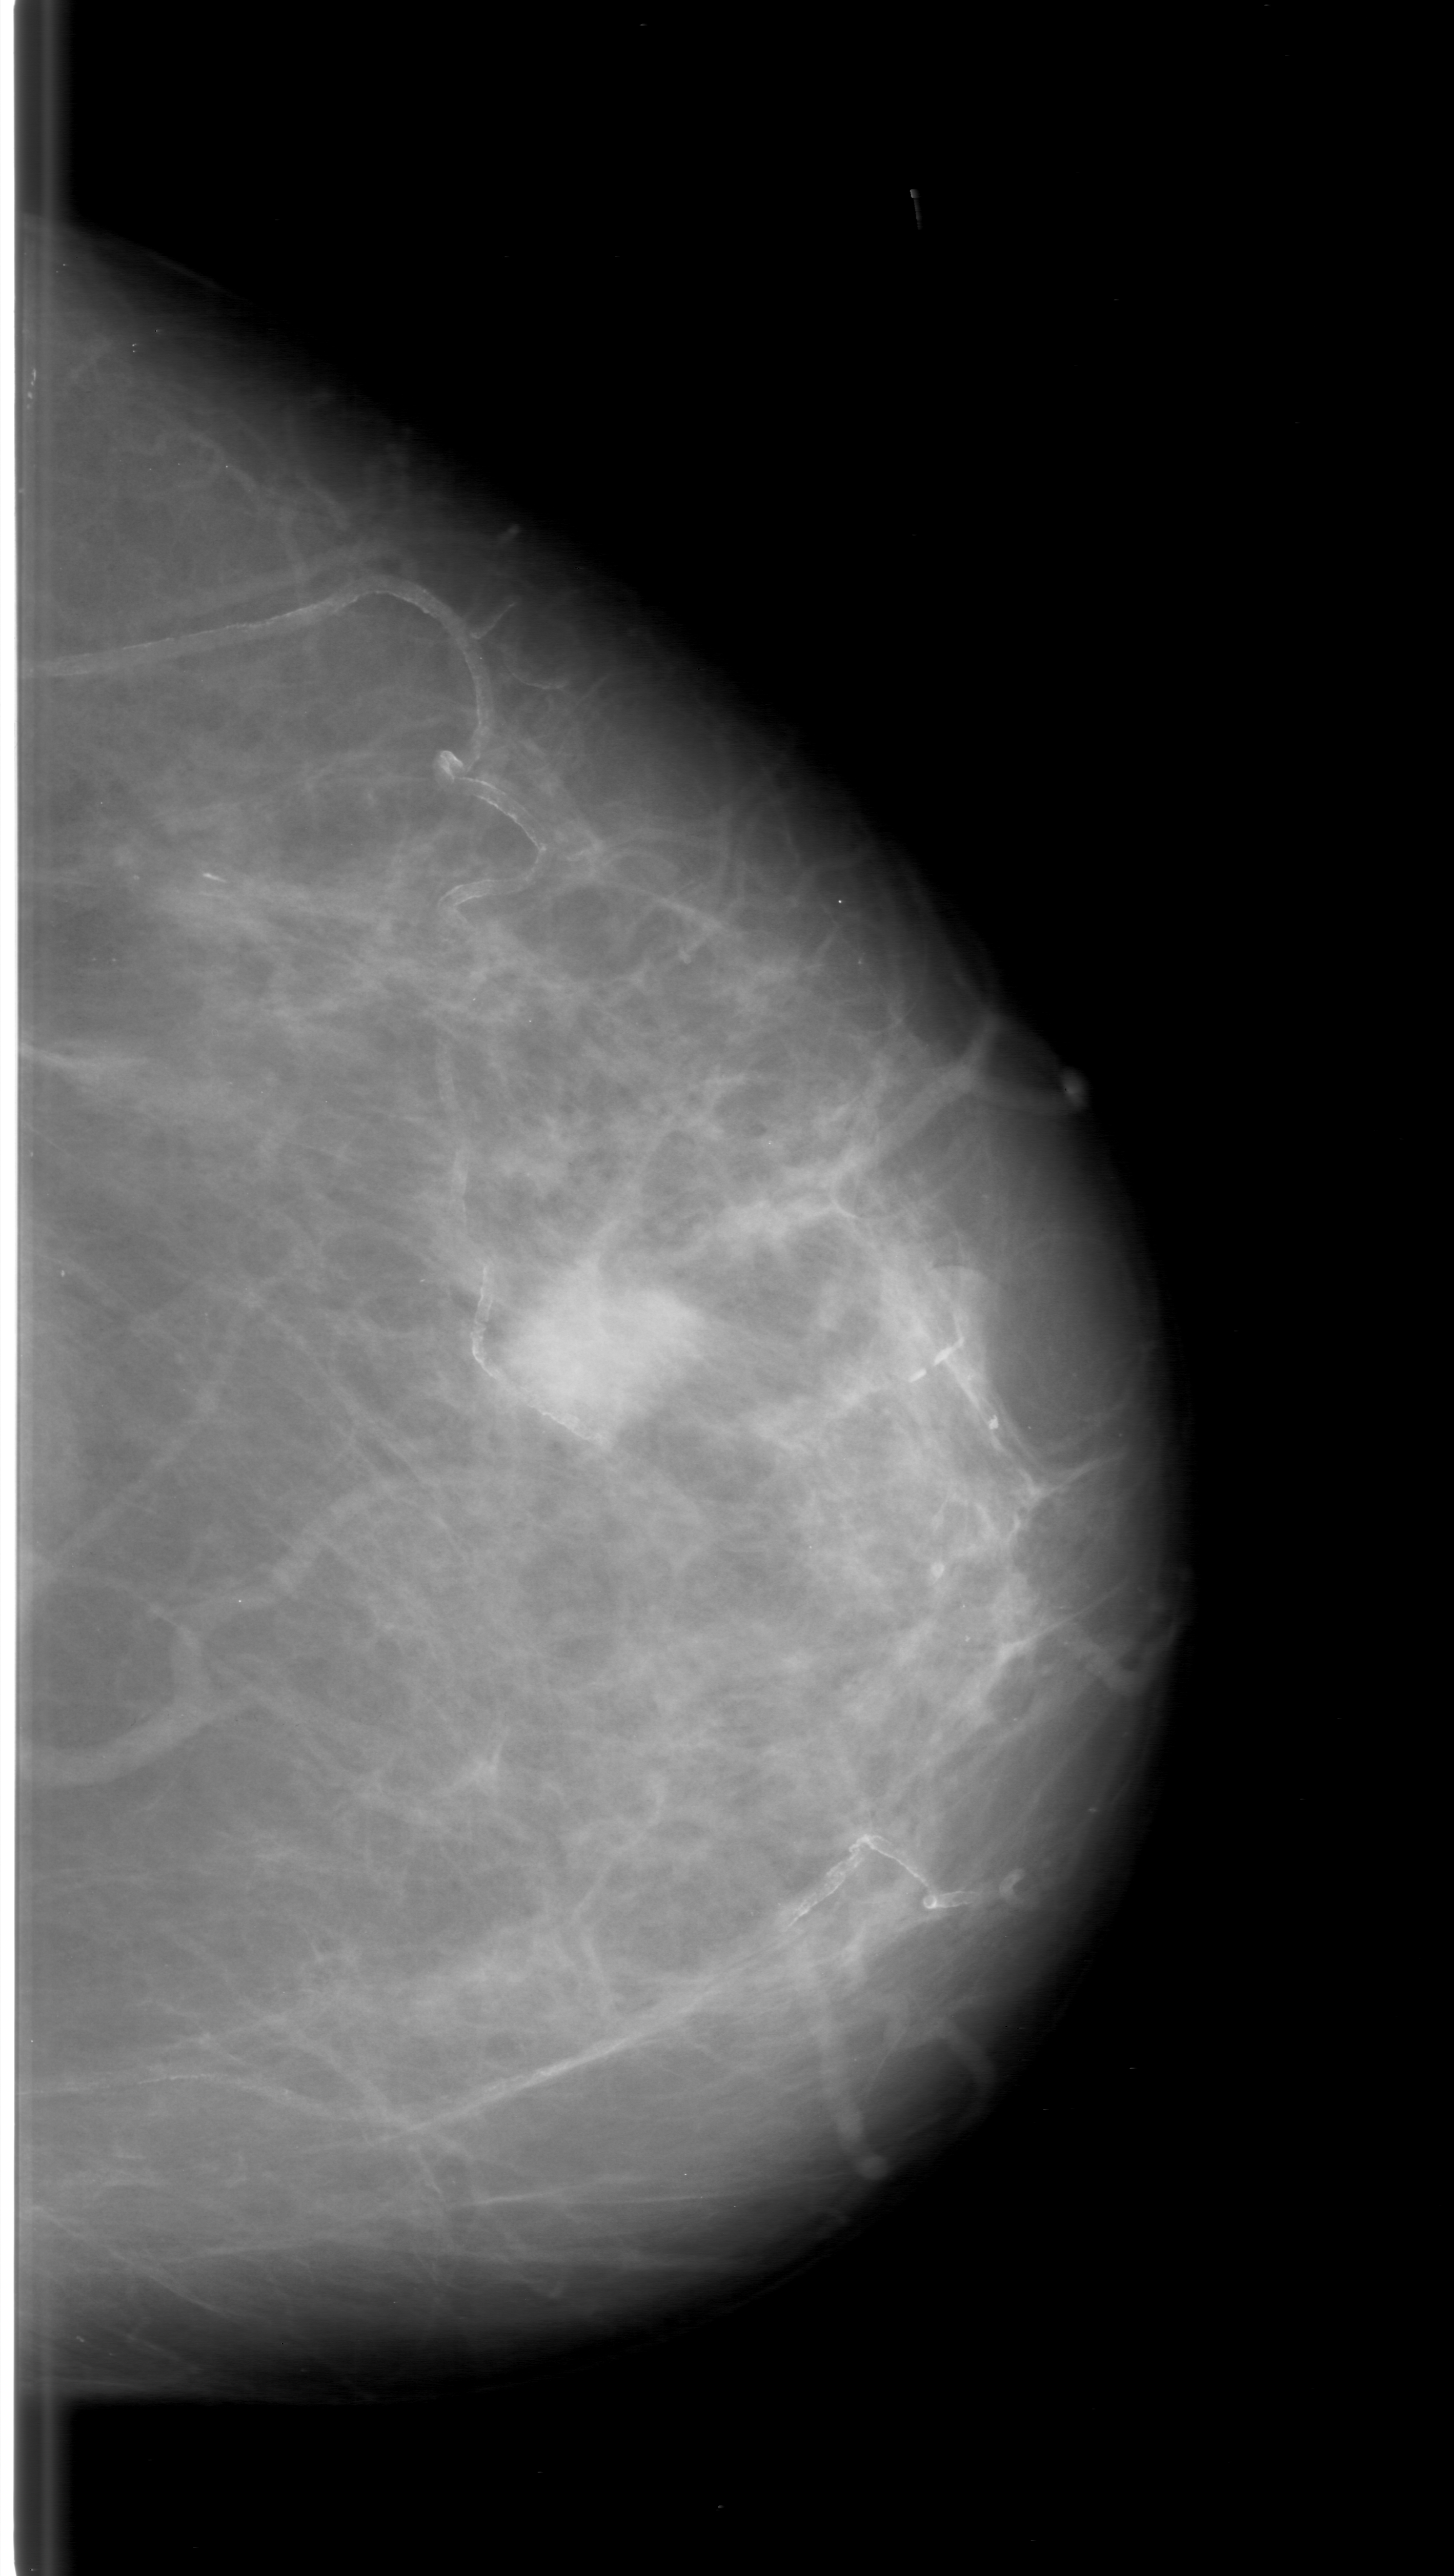
Mammogram (digitized film), left breast, craniocaudal (CC) view.
Marked abnormality: mass, shape oval, margins ill defined; BI-RADS assessment category 3; subtlety rating 4 on a 1 (subtle) to 5 (obvious) scale; pathology result (as recorded, not read from the image): malignant.